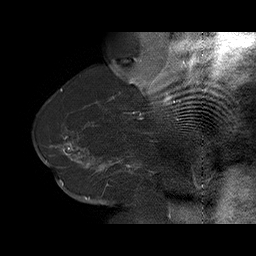
Breast MRI (dynamic contrast-enhanced), one sagittal slice; slice 47 of 75 in the series (ordered by position); dynamic contrast-enhanced series, time point 2 of 6 at this slice position (early post-contrast); 1.5 T; TE 4.5 ms, TR 32.4 ms; 3 mm slice thickness; 256 × 256 image matrix, field of view 180 × 180 mm. Female patient. Case-level facts recorded for this patient, not image findings: setting: breast cancer imaged before/during neoadjuvant chemotherapy; receptor status: HR-positive, HER2-negative.
Outlined on this slice (semi-automatic segmentation, software-assisted and operator-edited):
- analysis volume of interest (the breast-tissue region the enhancement analysis was run in; not a lesion): bounding box [x1, y1, x2, y2] px = [58, 134, 166, 191]
- tumour enhancement mask (voxels above the 100 % enhancement threshold inside the analysis volume of interest): [60, 137, 133, 171]